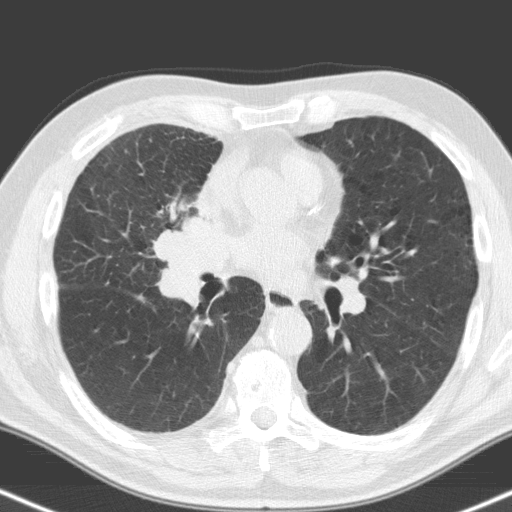
Low-dose screening chest CT, one axial slice. Slice 85 of 160 in the series (ordered by position). Lung window (W 1500 / L -600 HU). 3.2 mm slice thickness. 512 × 512 image matrix, field of view 324 × 324 mm.
Outlined on this slice (expert manual segmentation):
- lesion 1 (tumor, hilum of right lung): bounding box (x1, y1, x2, y2) in pixels: (156, 191, 238, 303)